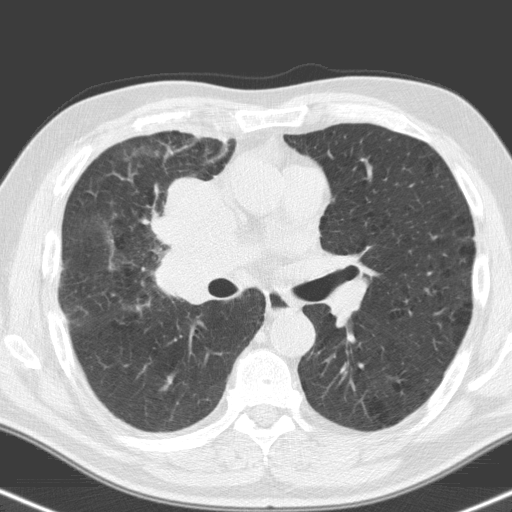
Low-dose screening chest CT, one axial slice. Position 92 of 160 along the scan axis. 120 kVp. Lung window (W 1500 / L -600 HU). 512 × 512 image matrix, field of view 324 × 324 mm.
Outlined on this slice (manually delineated by an expert):
- lesion 1 (tumor, hilum of right lung): box from (x=156, y=179) to (x=237, y=304) px